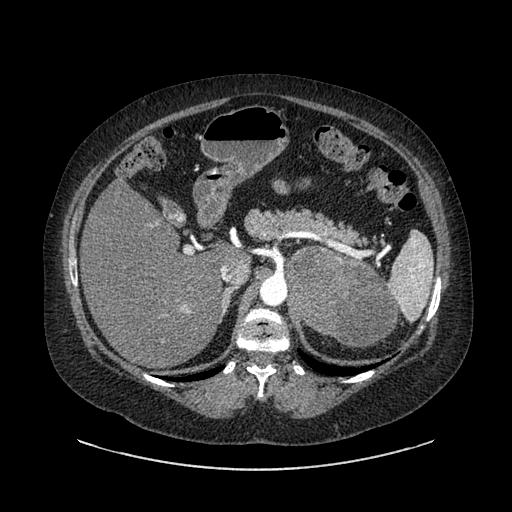
Contrast-enhanced abdominal CT, one axial slice. Position 589 of 769 along the scan axis. 120 kVp. Intravenous contrast given. Soft-tissue window (W 400 / L 40 HU). 0.62 mm slice thickness. 512 × 512 image matrix, field of view 460 × 460 mm. Patient: female, 61 years. Case-level facts recorded for this patient, not image findings: diagnosis: adrenocortical carcinoma; tumour side: left adrenal; tumour size at pathology: 13 cm; Ki-67 index: 79 %; stage (as recorded): 2.
Annotated regions visible in this slice (semi-automatic segmentation, software-assisted and operator-edited):
- mass: bounding box [x1, y1, x2, y2] px = [288, 248, 396, 345]